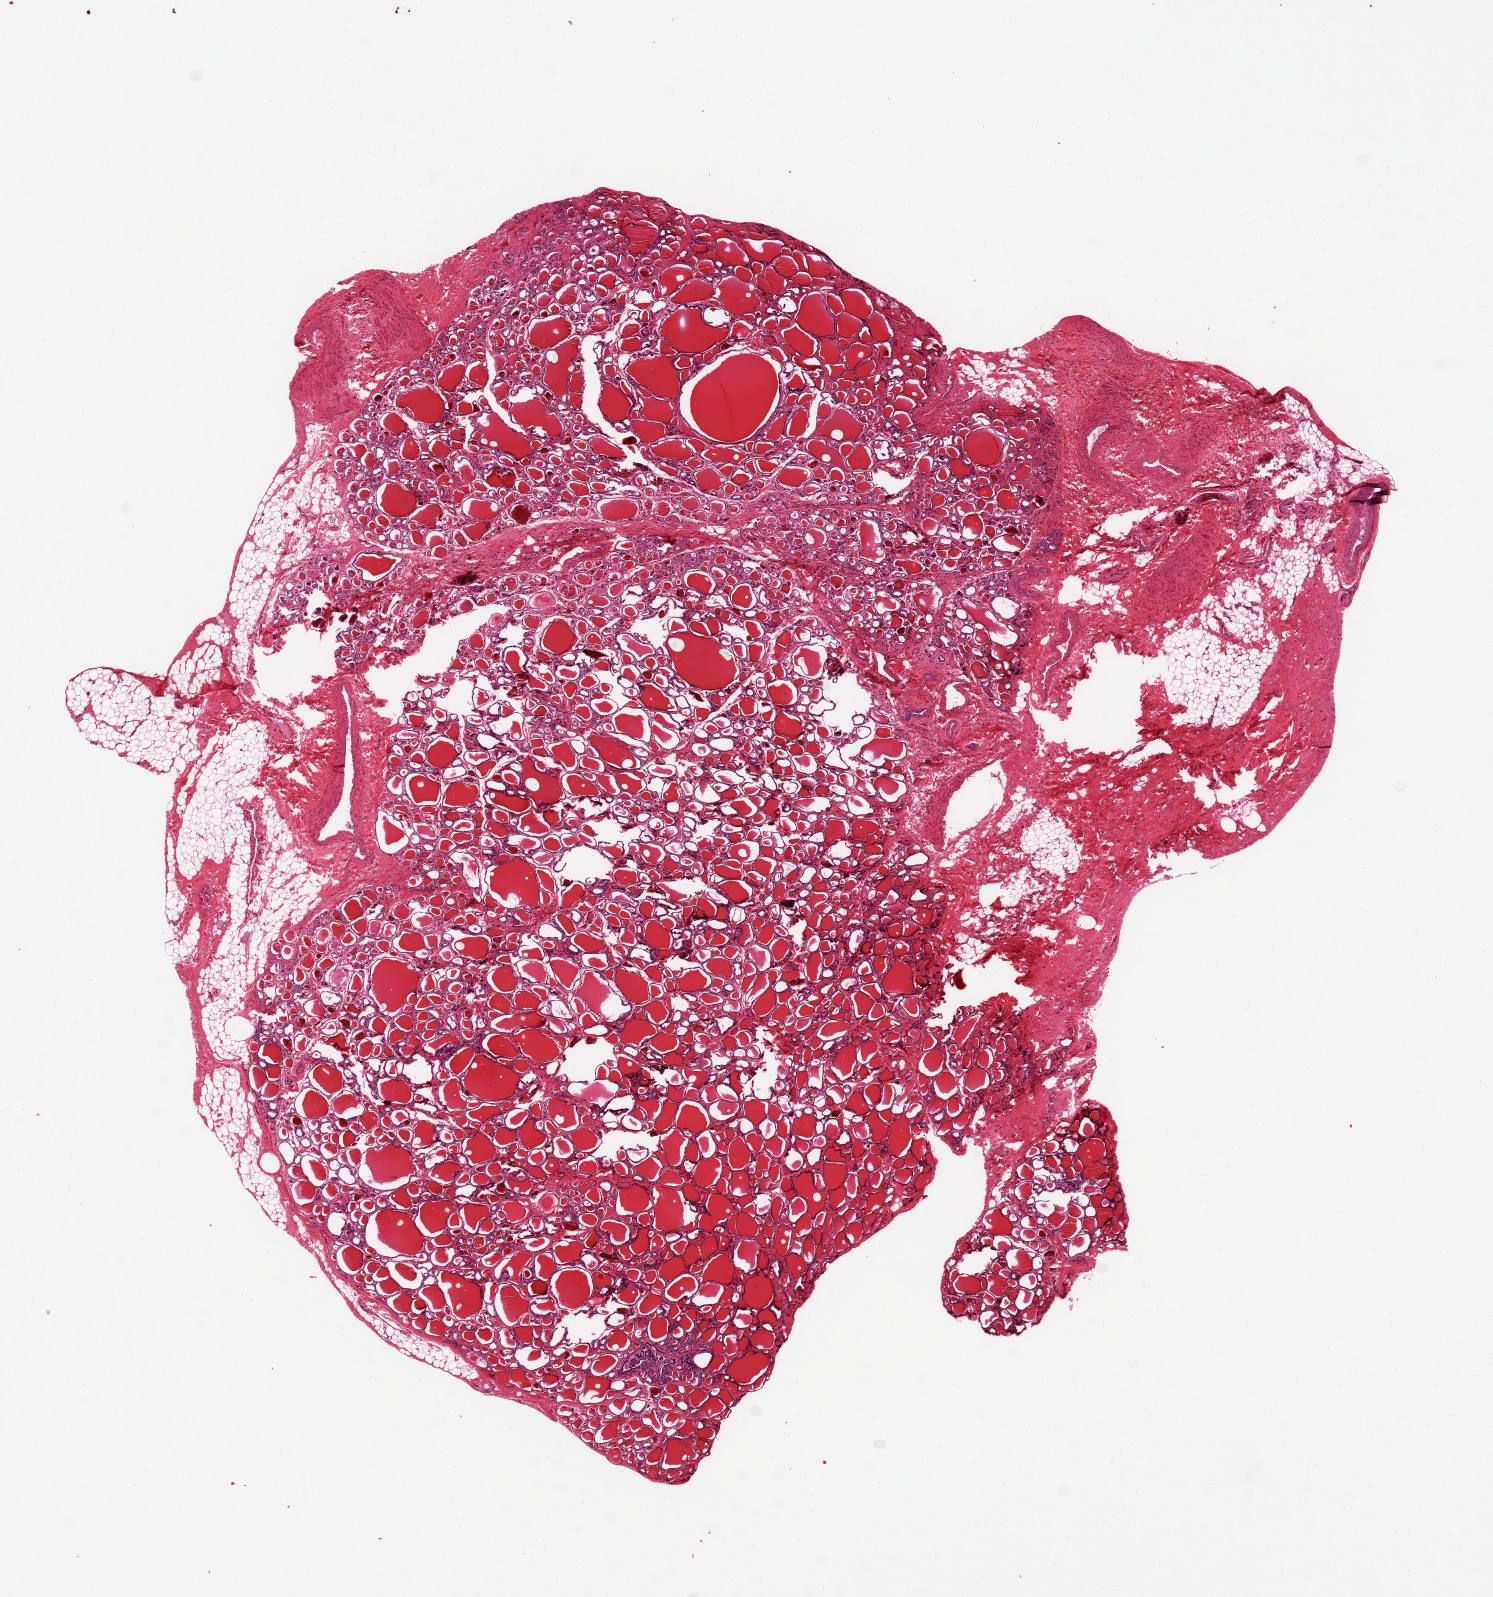
Haematoxylin and eosin whole-slide image, shown as a low-resolution overview of the whole scanned area (about 11.8 x 12.6 mm, acquisition: 20x scan). PAXgene-fixed, paraffin-embedded tissue. Section of thyroid (target tissue). Tissue donor sample.
* reviewer comment on this tissue sample: Possible 0.4 x 0.6mm occult papillary ca, pending slide review. Patchy areas of peripheral adipose tissue are poorly fixed, tears and holes in section